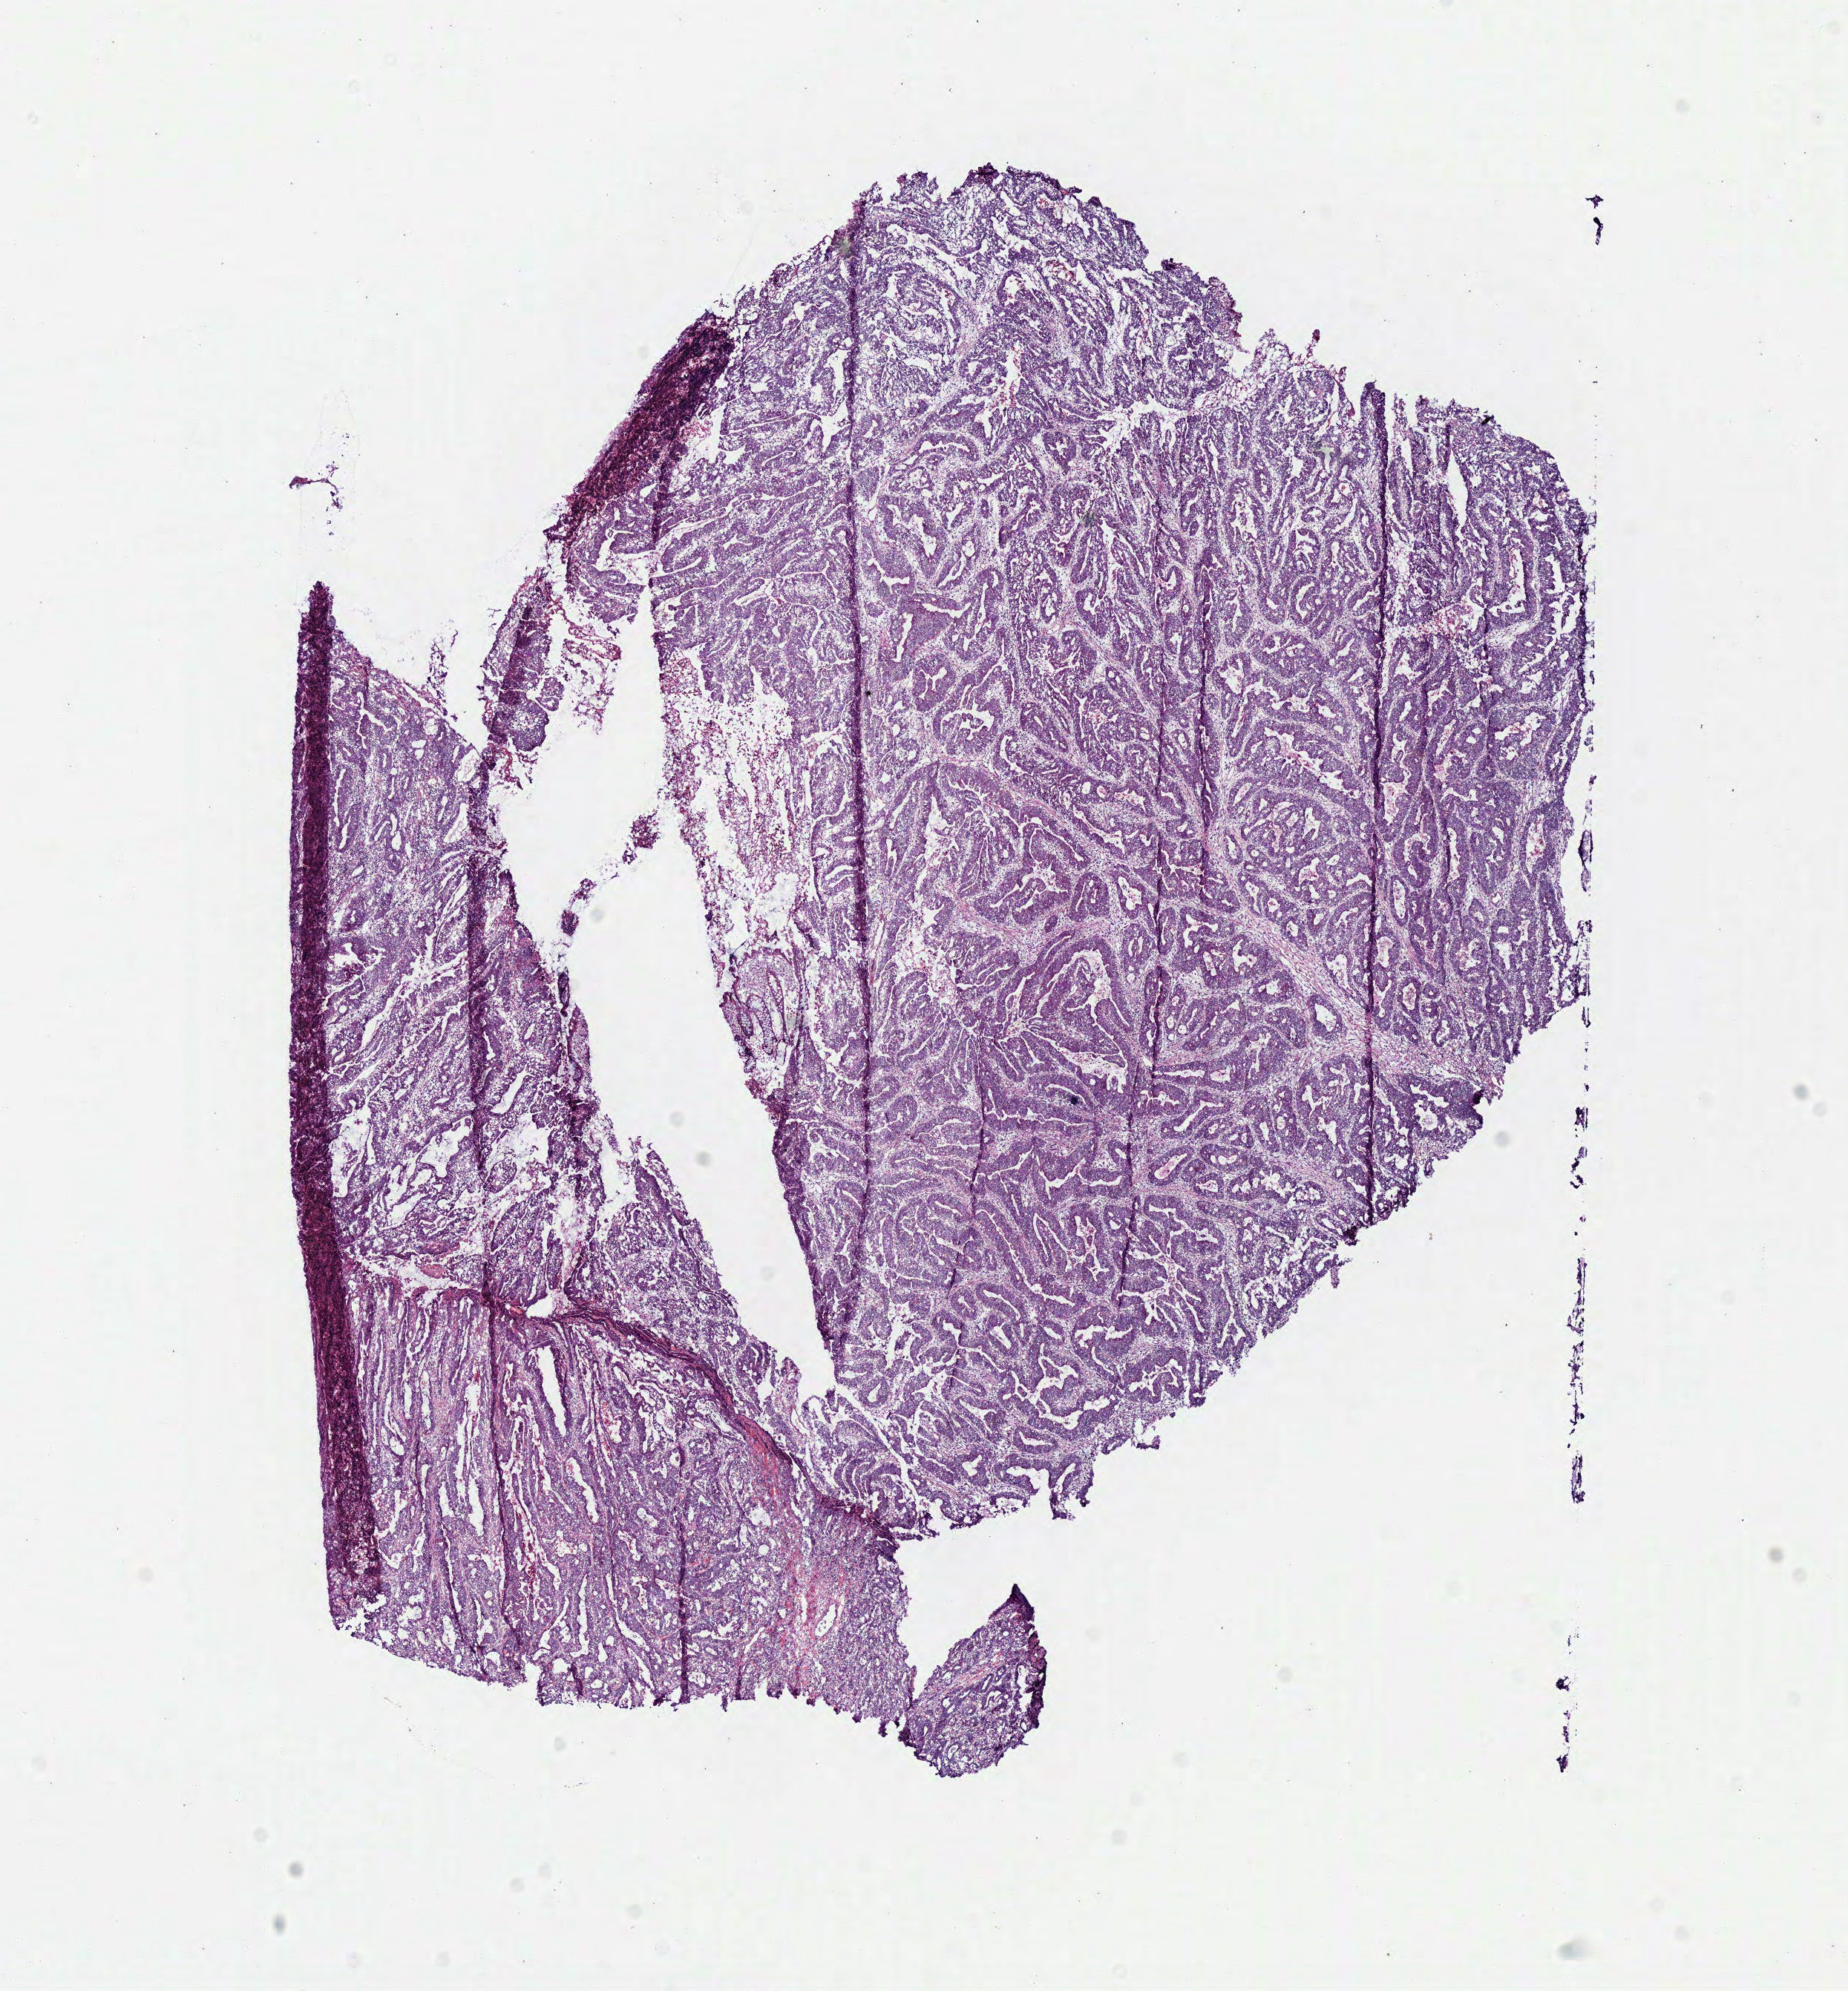
Digitized Hematoxylin and eosin (H&E) stained tissue section (whole slide), low-resolution overview of the scanned area, about 9.8 x 10.5 mm; frozen section; primary tumour sample from the colon. Female, age 40 years at initial diagnosis.
Pathologic diagnosis: Adenocarcinoma, NOS (sigmoid colon).